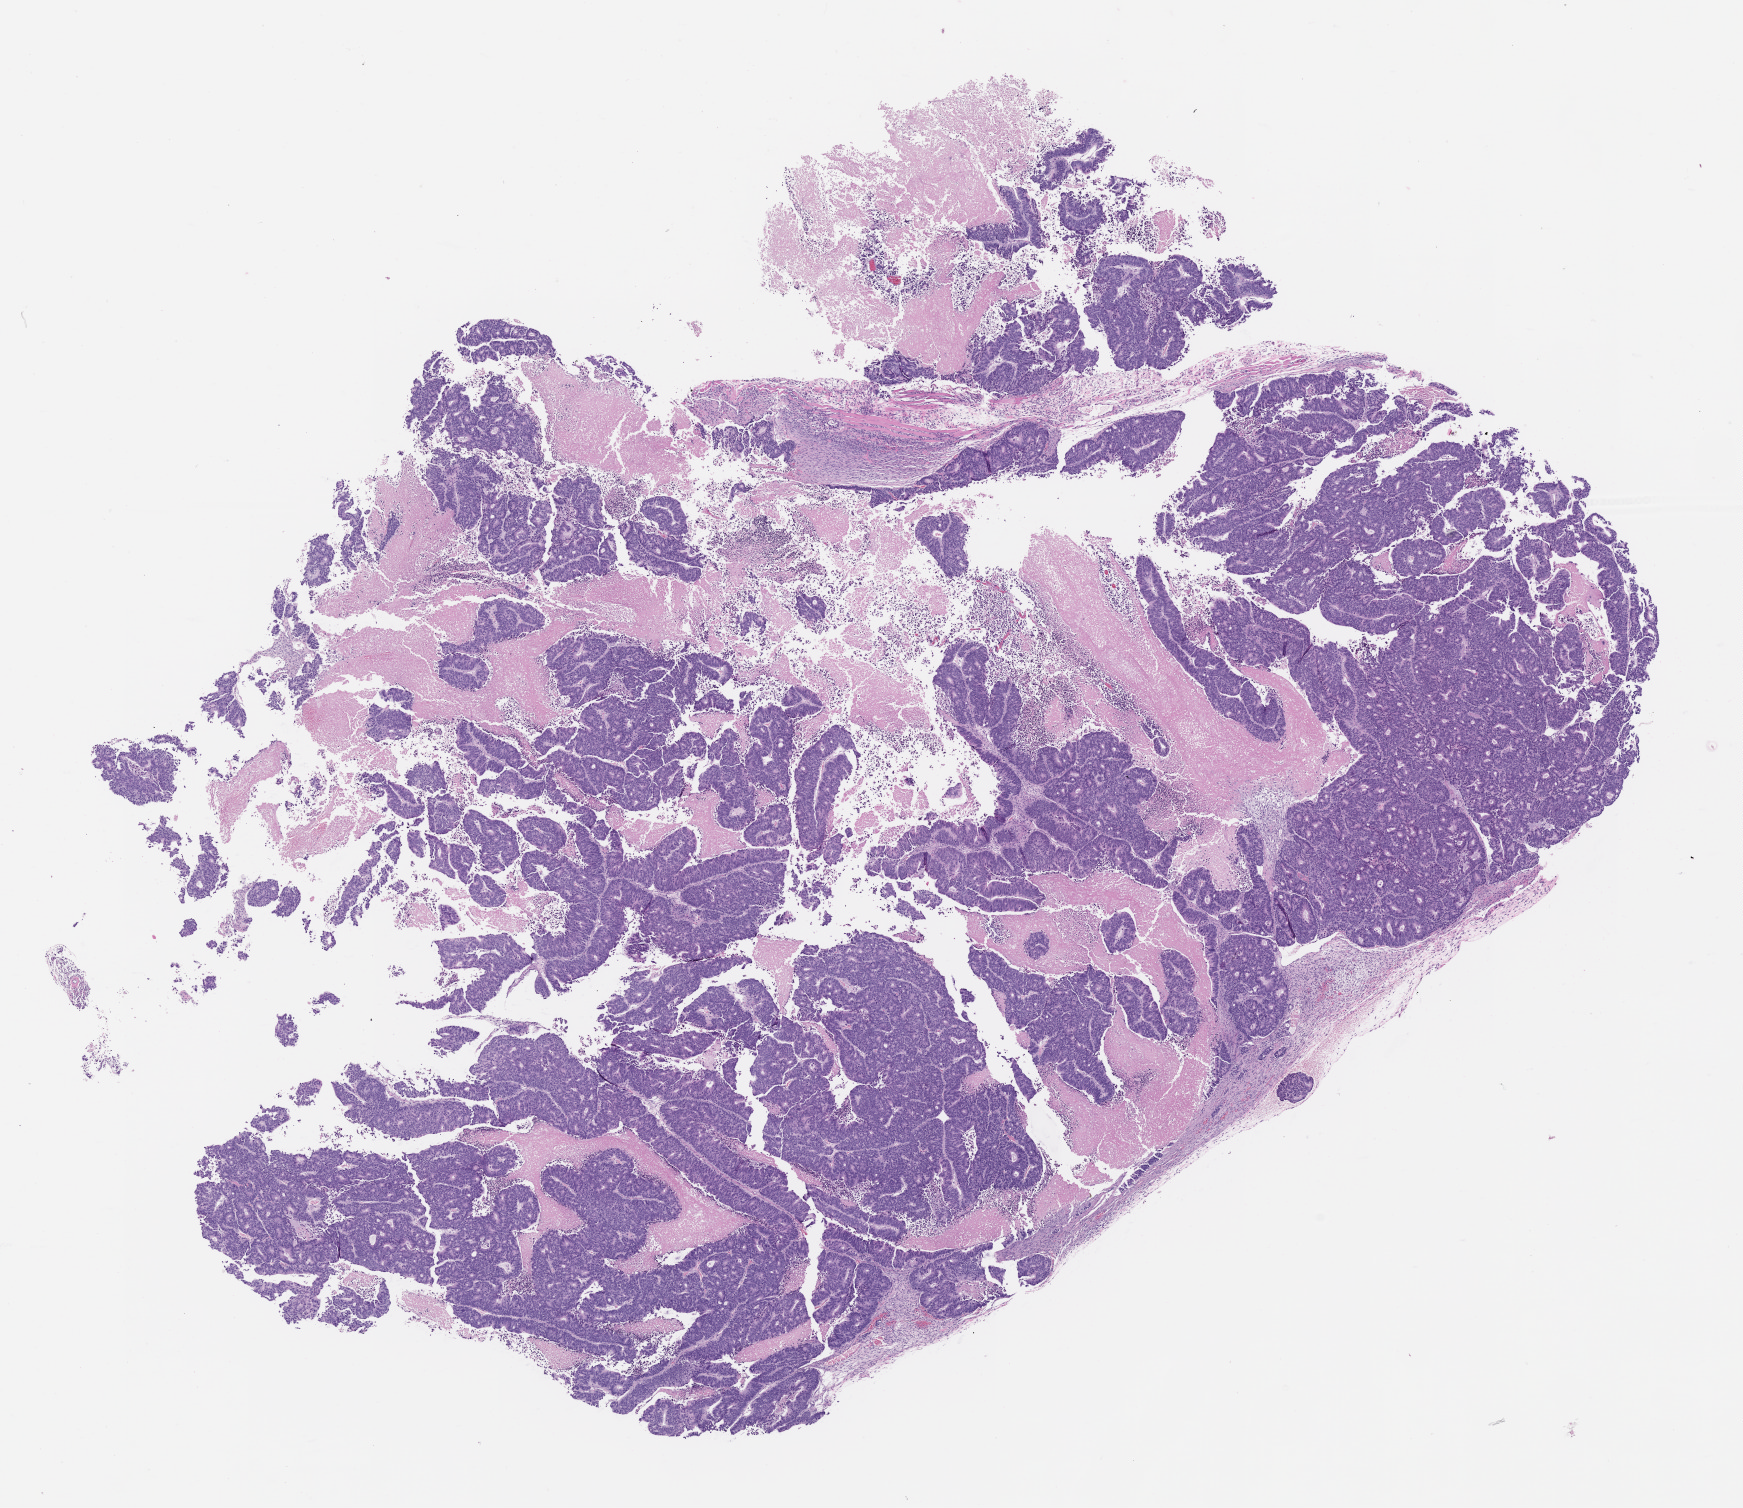
Whole-slide image, haematoxylin and eosin: patient-derived xenograft (human tumor grown in a mouse), passage 1 — shown as a low-resolution overview of the whole scanned area (about 14.0 x 12.1 mm), formalin-fixed paraffin-embedded section, originating tumor site category: colon.
Originating patient diagnosis: Colon Adenocarcinoma.